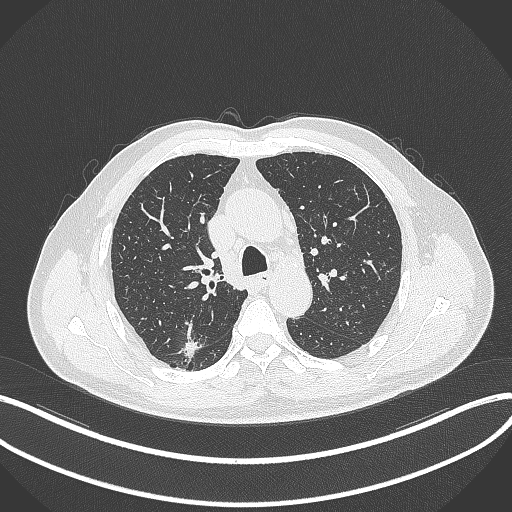
Chest CT, one axial slice. Position 256 of 359 along the scan axis. Lung window (W 1500 / L -600 HU). 1 mm slice thickness. 512 × 512 image matrix, field of view 400 × 400 mm. Patient: male, 69 years. Case-level facts recorded for this patient, not image findings: clinical TNM (as recorded): T1b N0 M0; histopathological grade: G2-3.
Annotated regions visible in this slice (rectangle marked by the reading radiologist):
- lung tumour (recorded histology: adenocarcinoma): bounding box (x1, y1, x2, y2) in pixels: (180, 338, 204, 364)